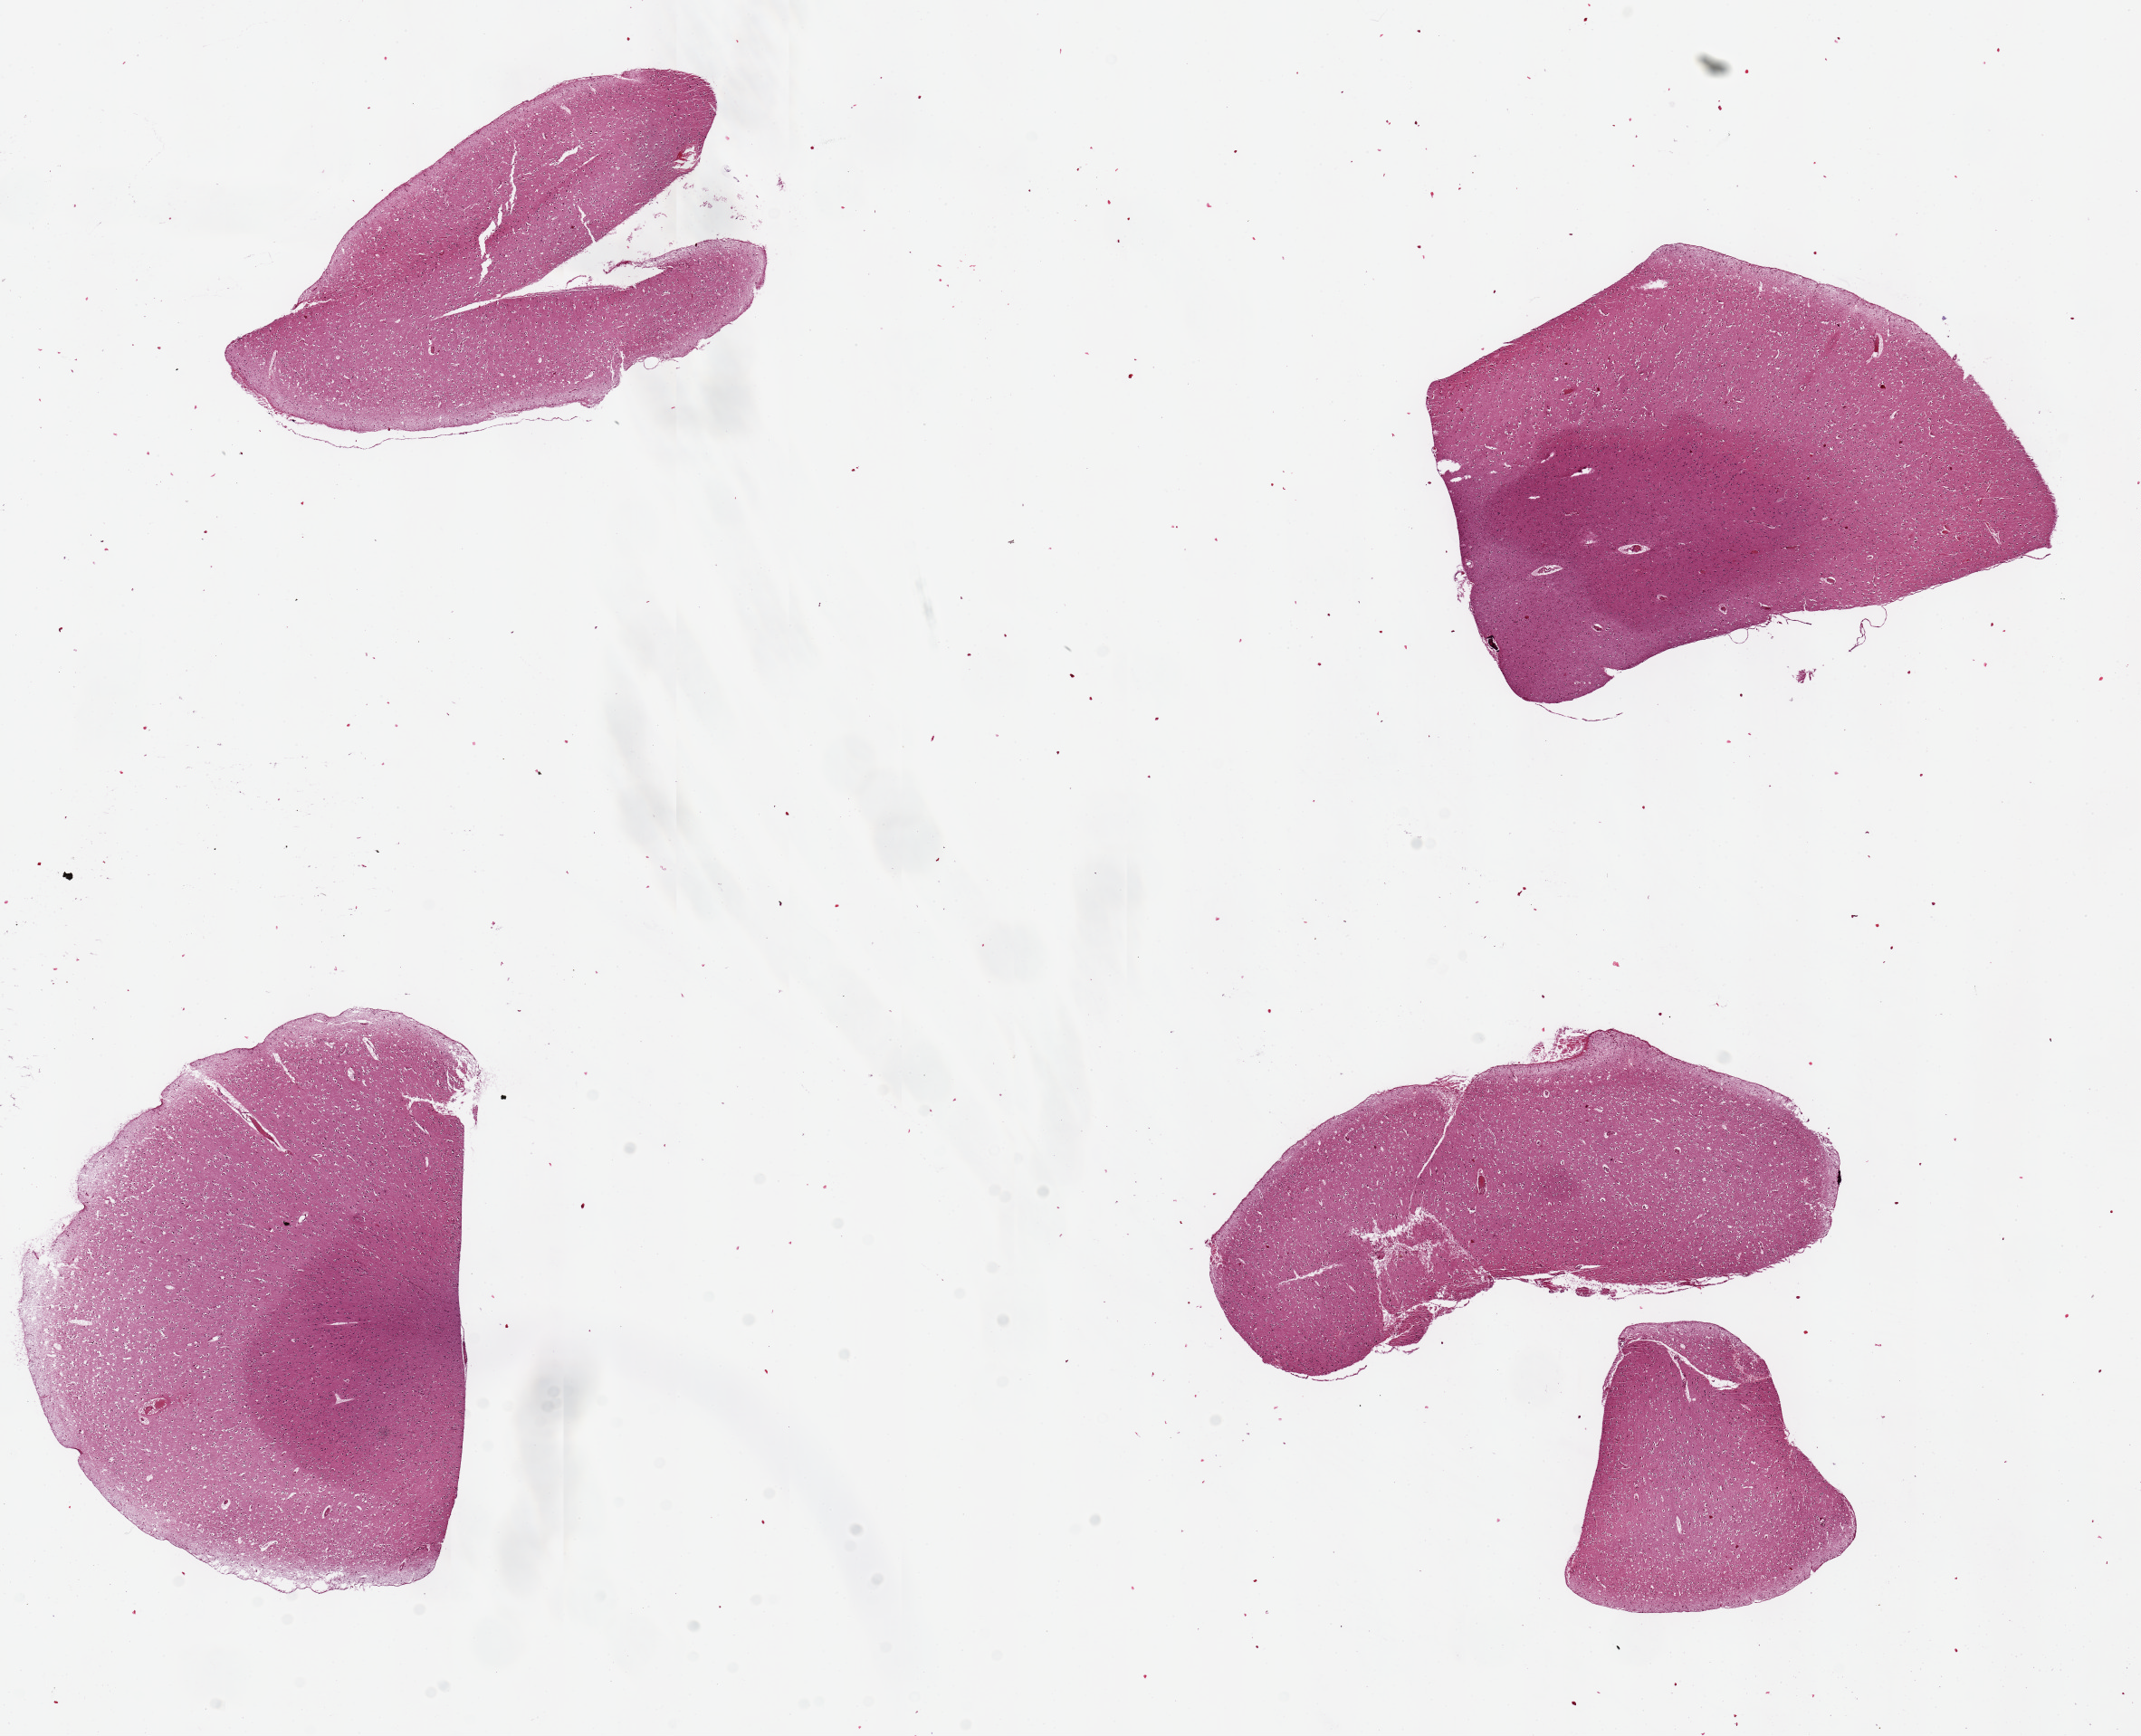
Digitized hematoxylin and eosin (H&E)-stained section — a low-resolution overview of the entire scanned area, about 18.7 x 15.2 mm. PAXgene-fixed, paraffin-embedded tissue. Section of cerebral cortex (target tissue). Tissue donor sample. Donor: male.
Review note (as recorded): 4 pieces, up to 5.5x5mm.